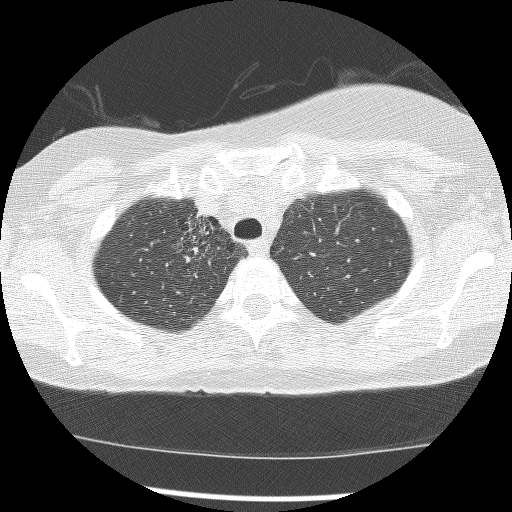
Low-dose screening chest CT, axial slice; baseline annual screen; lung window (W 1500 / L -600 HU); 2.5 mm slice thickness; slice 30 of 172 in the series. Female participant, aged 56 years at enrolment. Current smoker at enrolment.
Lesion marked by an expert reader, box from (x=166, y=212) to (x=226, y=279) px. The screening reader recorded 2 non-calcified nodules or masses ≥4 mm on this exam; which of them this box marks is not recorded. Official screen result: positive, change unspecified: nodule(s) >= 4 mm or enlarging nodule(s), mass(es), or other non-specific abnormalities suspicious for lung cancer. Participant outcome: lung cancer diagnosed 1185 days after this screen — adenocarcinoma, NOS, right upper lobe, stage IIIB (AJCC 6th edition), 8 mm at pathology.